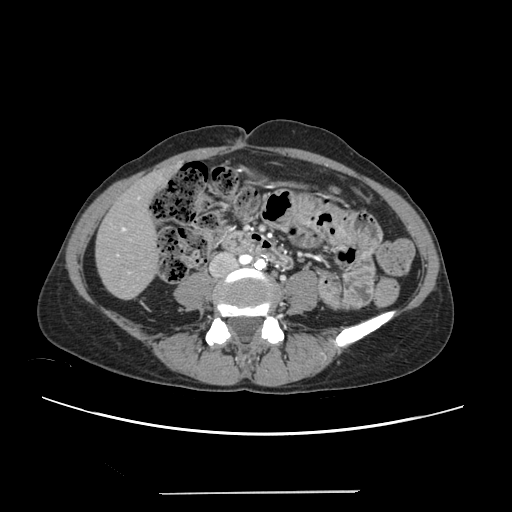
Contrast-enhanced abdominal CT, one axial slice. Slice 48 of 240 in the series (ordered by position). Soft-tissue window (W 400 / L 40 HU). 1.25 mm slice thickness. 512 × 512 image matrix, field of view 371 × 371 mm. Female patient, age 60 years. Case-level facts recorded for this patient, not image findings: diagnosis: colorectal cancer liver metastases, imaged before liver resection; multiple liver metastases: no.
Structures marked on this image (manually delineated by an expert):
- liver: bounding box [x1, y1, x2, y2] px = [97, 169, 172, 298]
- planned liver remnant (the part of the liver to remain after resection): [97, 171, 168, 298]
- portal vein (with intrahepatic branches): [116, 196, 140, 274]